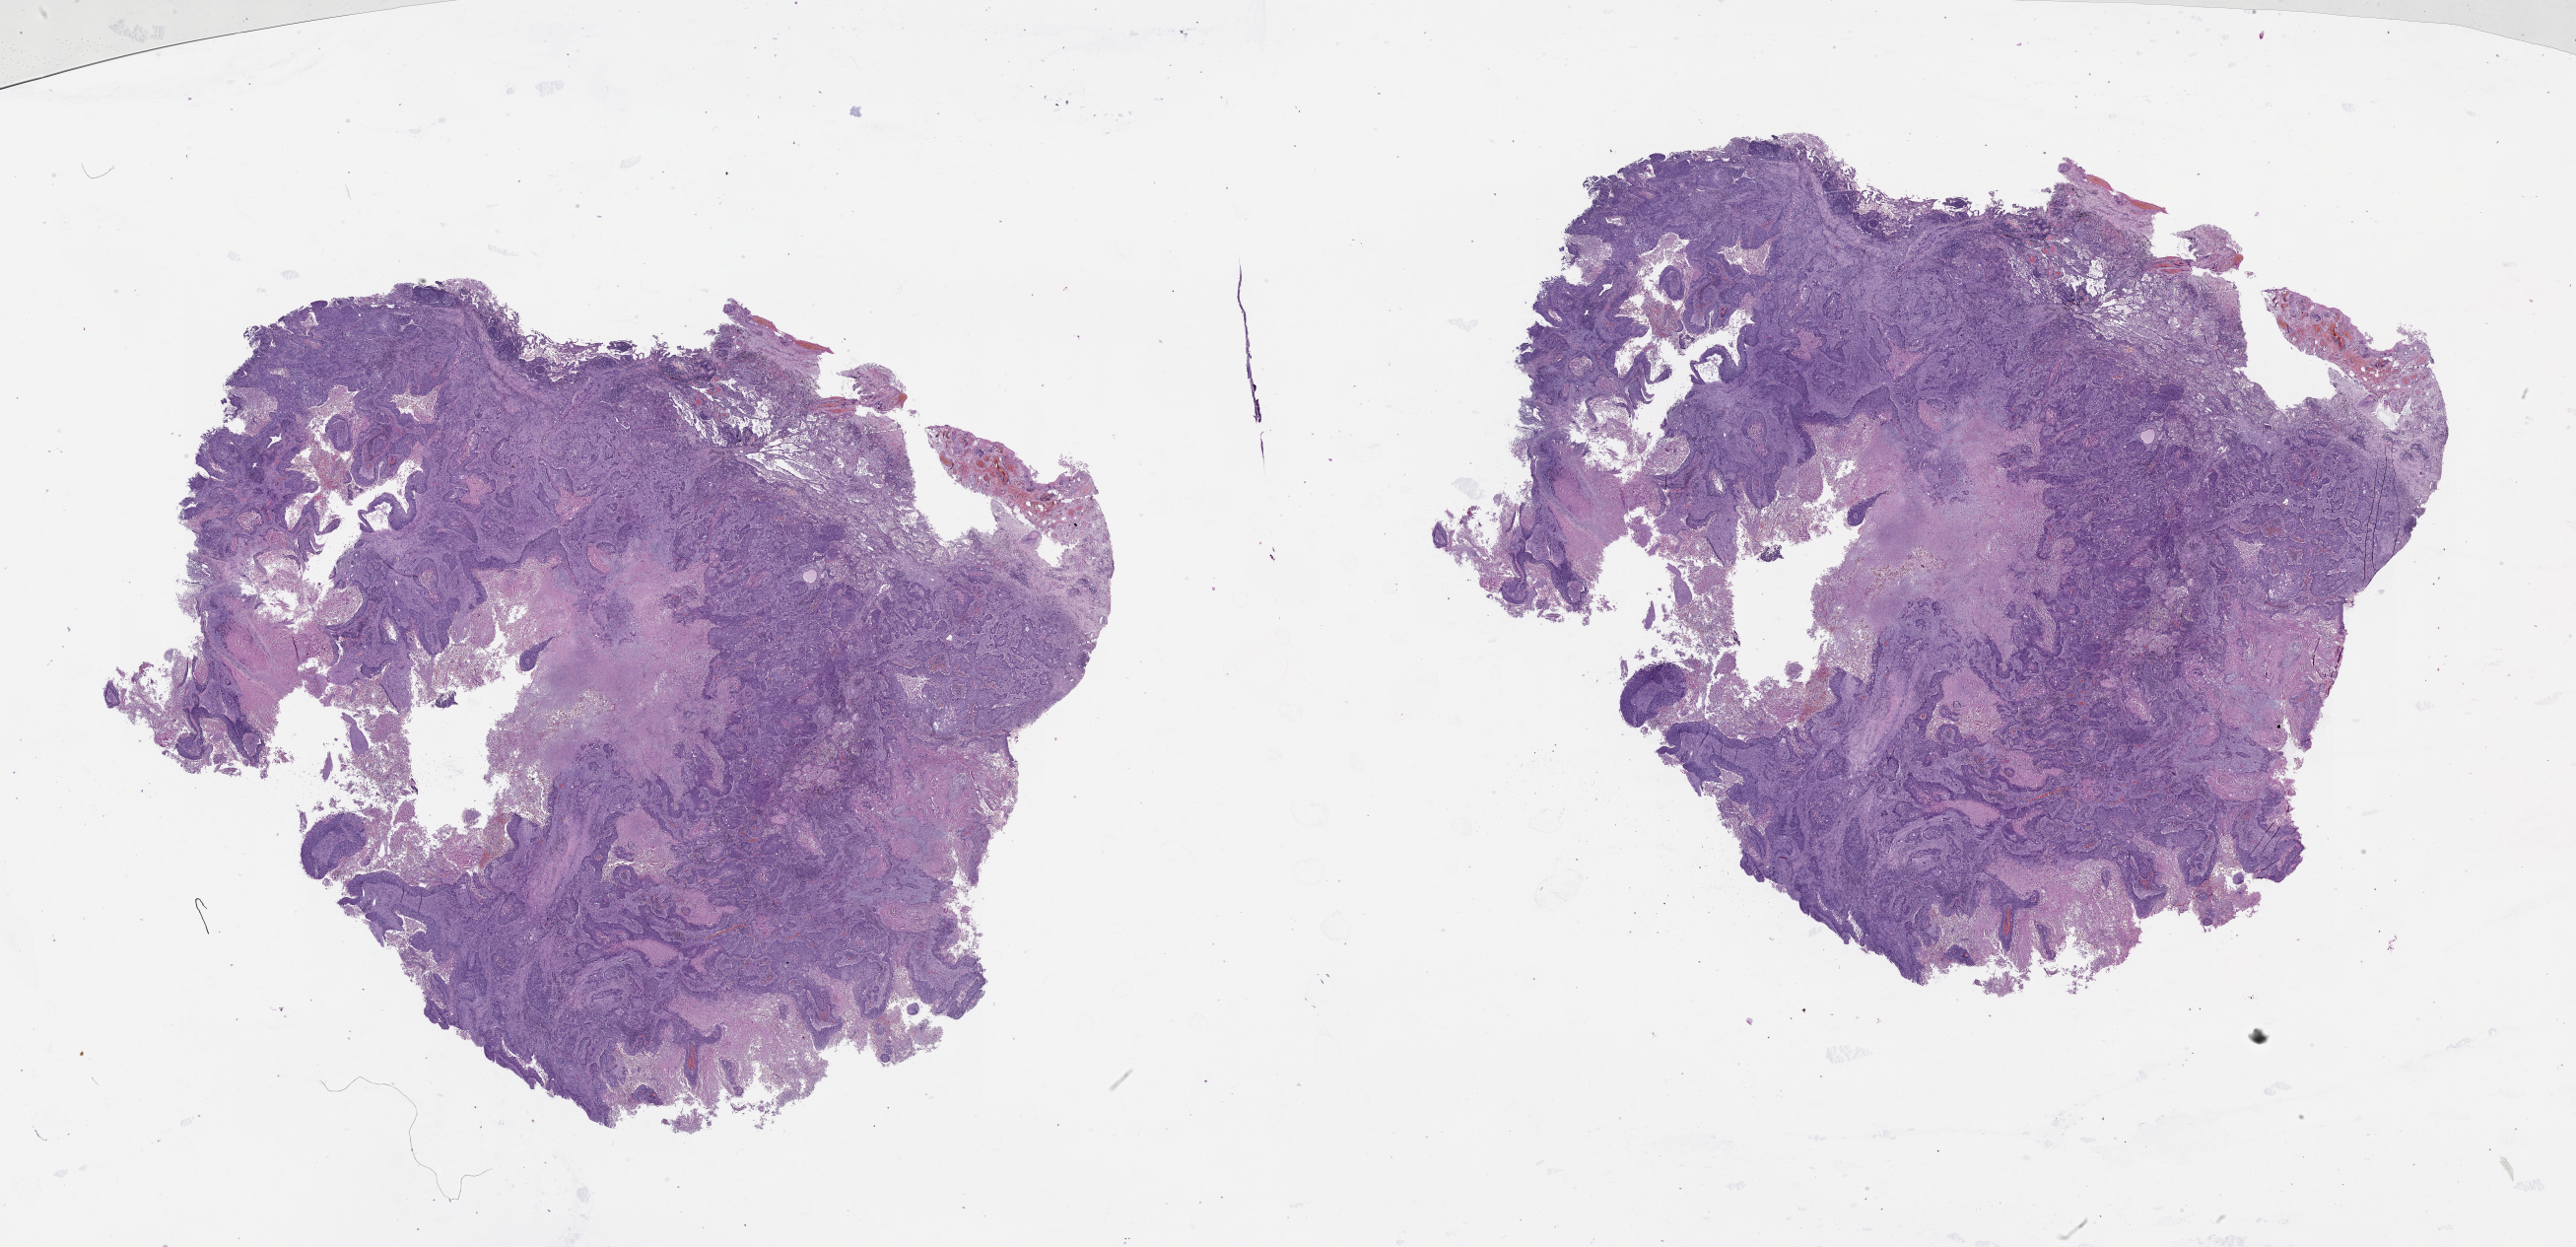
Digitized Hematoxylin and eosin (H&E) stained tissue section (whole slide) — low-resolution overview of the scanned area, about 42.1 x 20.4 mm (slide scanned at 20x); lung, tumour tissue. Patient: male, age 57 years.
* patient diagnosis (cohort enrolment): squamous cell carcinoma (lung)